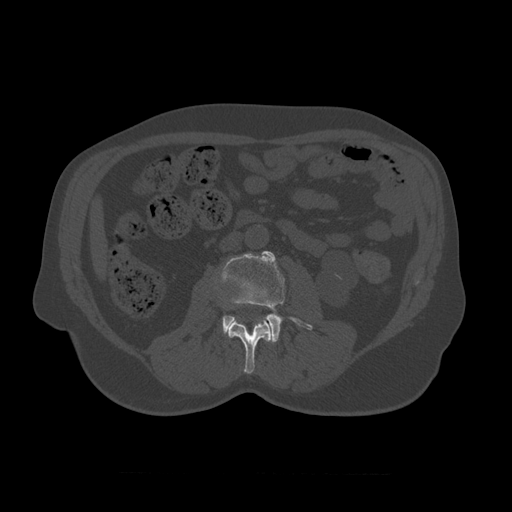
CT including the spine, one axial slice. Position 317 of 450 along the scan axis. Reconstruction kernel STANDARD. 120 kVp. Bone window (W 1800 / L 400 HU). 1.25 mm slice thickness. 512 × 512 image matrix, field of view 405 × 405 mm. Patient age 75 years. Case-level facts recorded for this patient, not image findings: primary cancer: prostate.
Annotated regions visible in this slice (semi-automatic segmentation, software-assisted and operator-edited):
- L2 vertebra: bounding box <228,317,274,374> (left, top, right, bottom; pixels)
- L3 vertebra: <216,251,313,343>